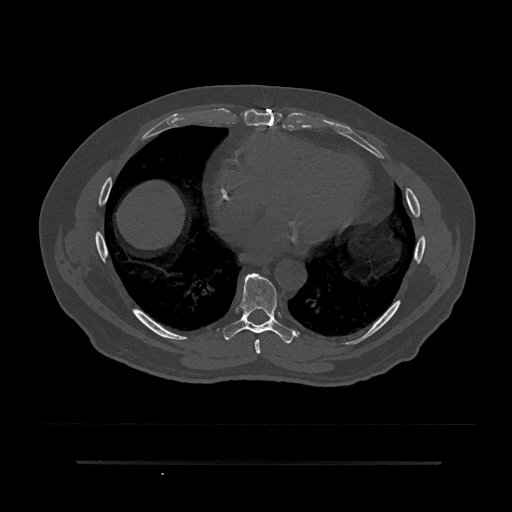
CT including the spine, one axial slice; slice 435 of 797 in the series (ordered by position); reconstruction kernel Br40s/3; 120 kVp; bone window (W 1800 / L 400 HU); 512 × 512 image matrix, field of view 464 × 464 mm. Male patient, age 59 years. Case-level facts recorded for this patient, not image findings: primary cancer: bile ducts.
Structures marked on this image (semi-automatic segmentation, software-assisted and operator-edited):
- T7 vertebra: box from (x=255, y=339) to (x=260, y=354) px
- T8 vertebra: (x=223, y=273)–(x=295, y=344)